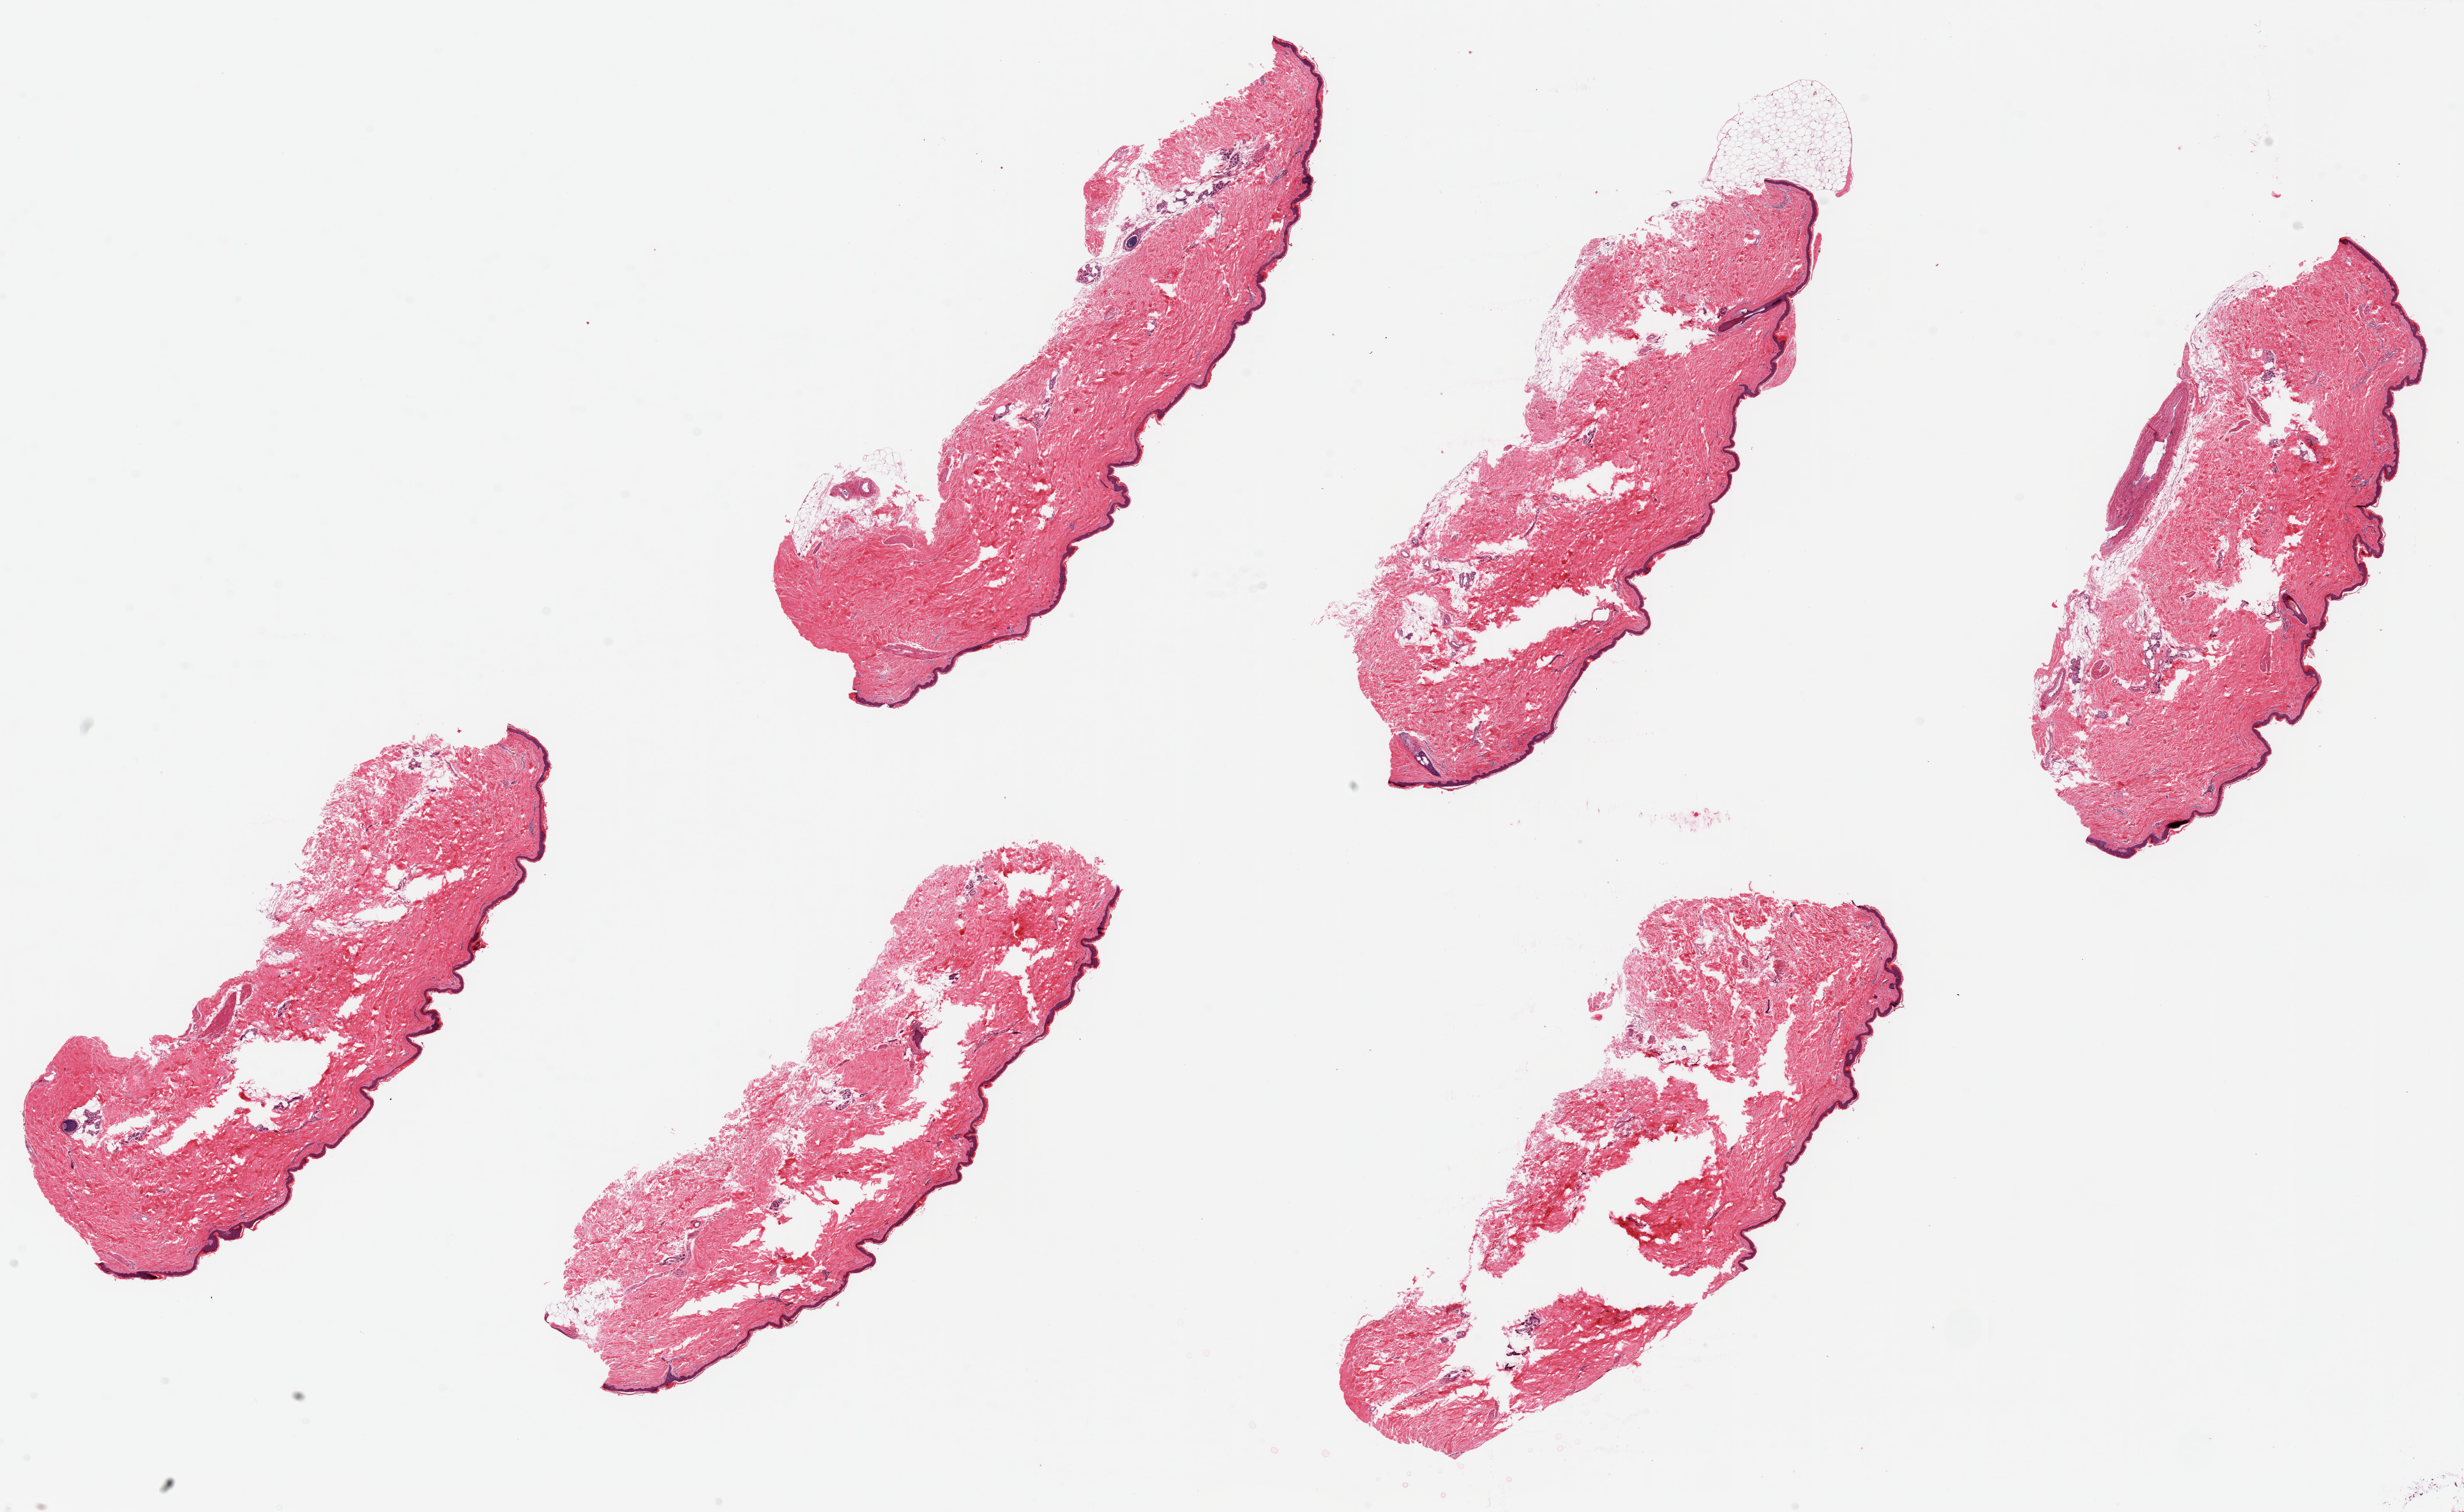
Digitized H&E-stained section — whole scanned area (about 30.5 x 18.7 mm, slide scanned at 20x) shown as a low-resolution overview. PAXgene-fixed, paraffin-embedded tissue. Sampled site (target tissue): skin of lower leg. Donor tissue sample. Donor: male.
- review note (as recorded): 6 pieces ~9x2.5mm, Squamous epithelium is 1-2% thickness